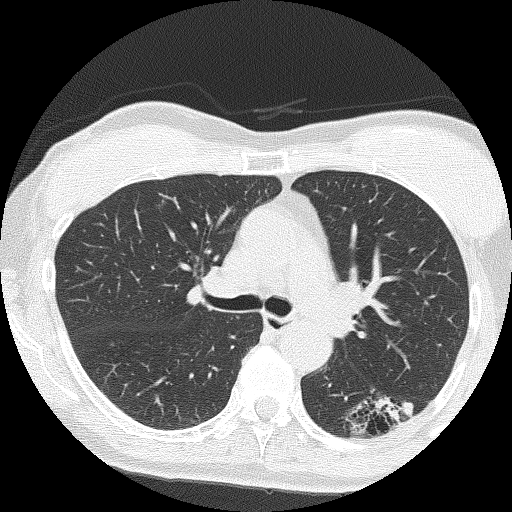
Chest CT (low-dose screening protocol), one axial image, second screening round (one year after baseline), lung window (W 1500 / L -600 HU), lung (sharp) reconstruction kernel (FC51), slice 59 of 159 in the series, 512 × 512 image matrix, field of view 303 × 303 mm. Female, age 64 years at enrolment. Former smoker at enrolment.
- Lesion marked by an expert reader, bounding box <355,383,424,439> (left, top, right, bottom; pixels).
- The screening reader recorded 3 non-calcified nodules or masses ≥4 mm on this exam (right upper lobe, right upper lobe, right middle lobe); which of them this box marks is not recorded.
- Official screen result: positive, other.